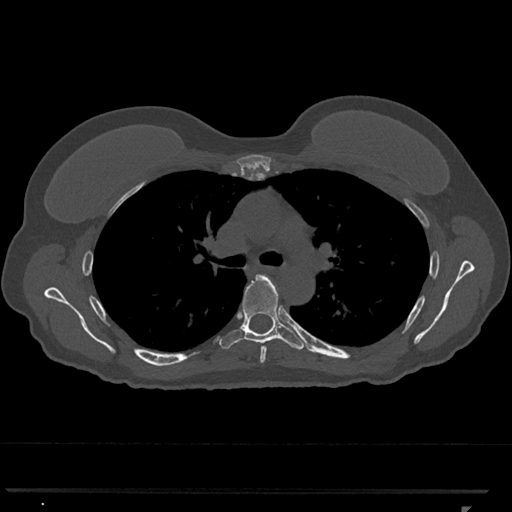
CT including the spine, one axial slice. Slice 773 of 793 in the series (ordered by position). Reconstruction kernel Br40s/3. 120 kVp. Bone window (W 1800 / L 400 HU). 512 × 512 image matrix. Female patient, age 62 years. From the clinical record (not read from this slice): primary cancer: renal.
Structures marked on this image (semi-automatic segmentation, software-assisted and operator-edited):
- T5 vertebra: bounding box [x1, y1, x2, y2] px = [260, 290, 278, 363]
- T6 vertebra: [219, 274, 305, 350]